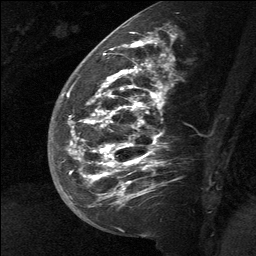
Breast MRI (dynamic contrast-enhanced), one sagittal slice. Slice 27 of 64 in the series (ordered by position). Dynamic contrast-enhanced study with each time point stored as its own series, time point 2 of 3 at this slice position (early post-contrast, ordered by acquisition time). 1.5 T. TE 4.8 ms, TR 27 ms. 256 × 256 image matrix, field of view 180 × 180 mm. Female patient, age 39 years. From the clinical record (not read from this slice): setting: breast cancer imaged before/during neoadjuvant chemotherapy; receptor status: HER2-positive.
Annotated regions visible in this slice (semi-automatic segmentation, software-assisted and operator-edited):
- analysis volume of interest (the breast-tissue region the enhancement analysis was run in; not a lesion): box from (x=58, y=40) to (x=170, y=217) px
- tumour enhancement mask (voxels above the 90 % enhancement threshold inside the analysis volume of interest): (x=67, y=40)–(x=155, y=198)